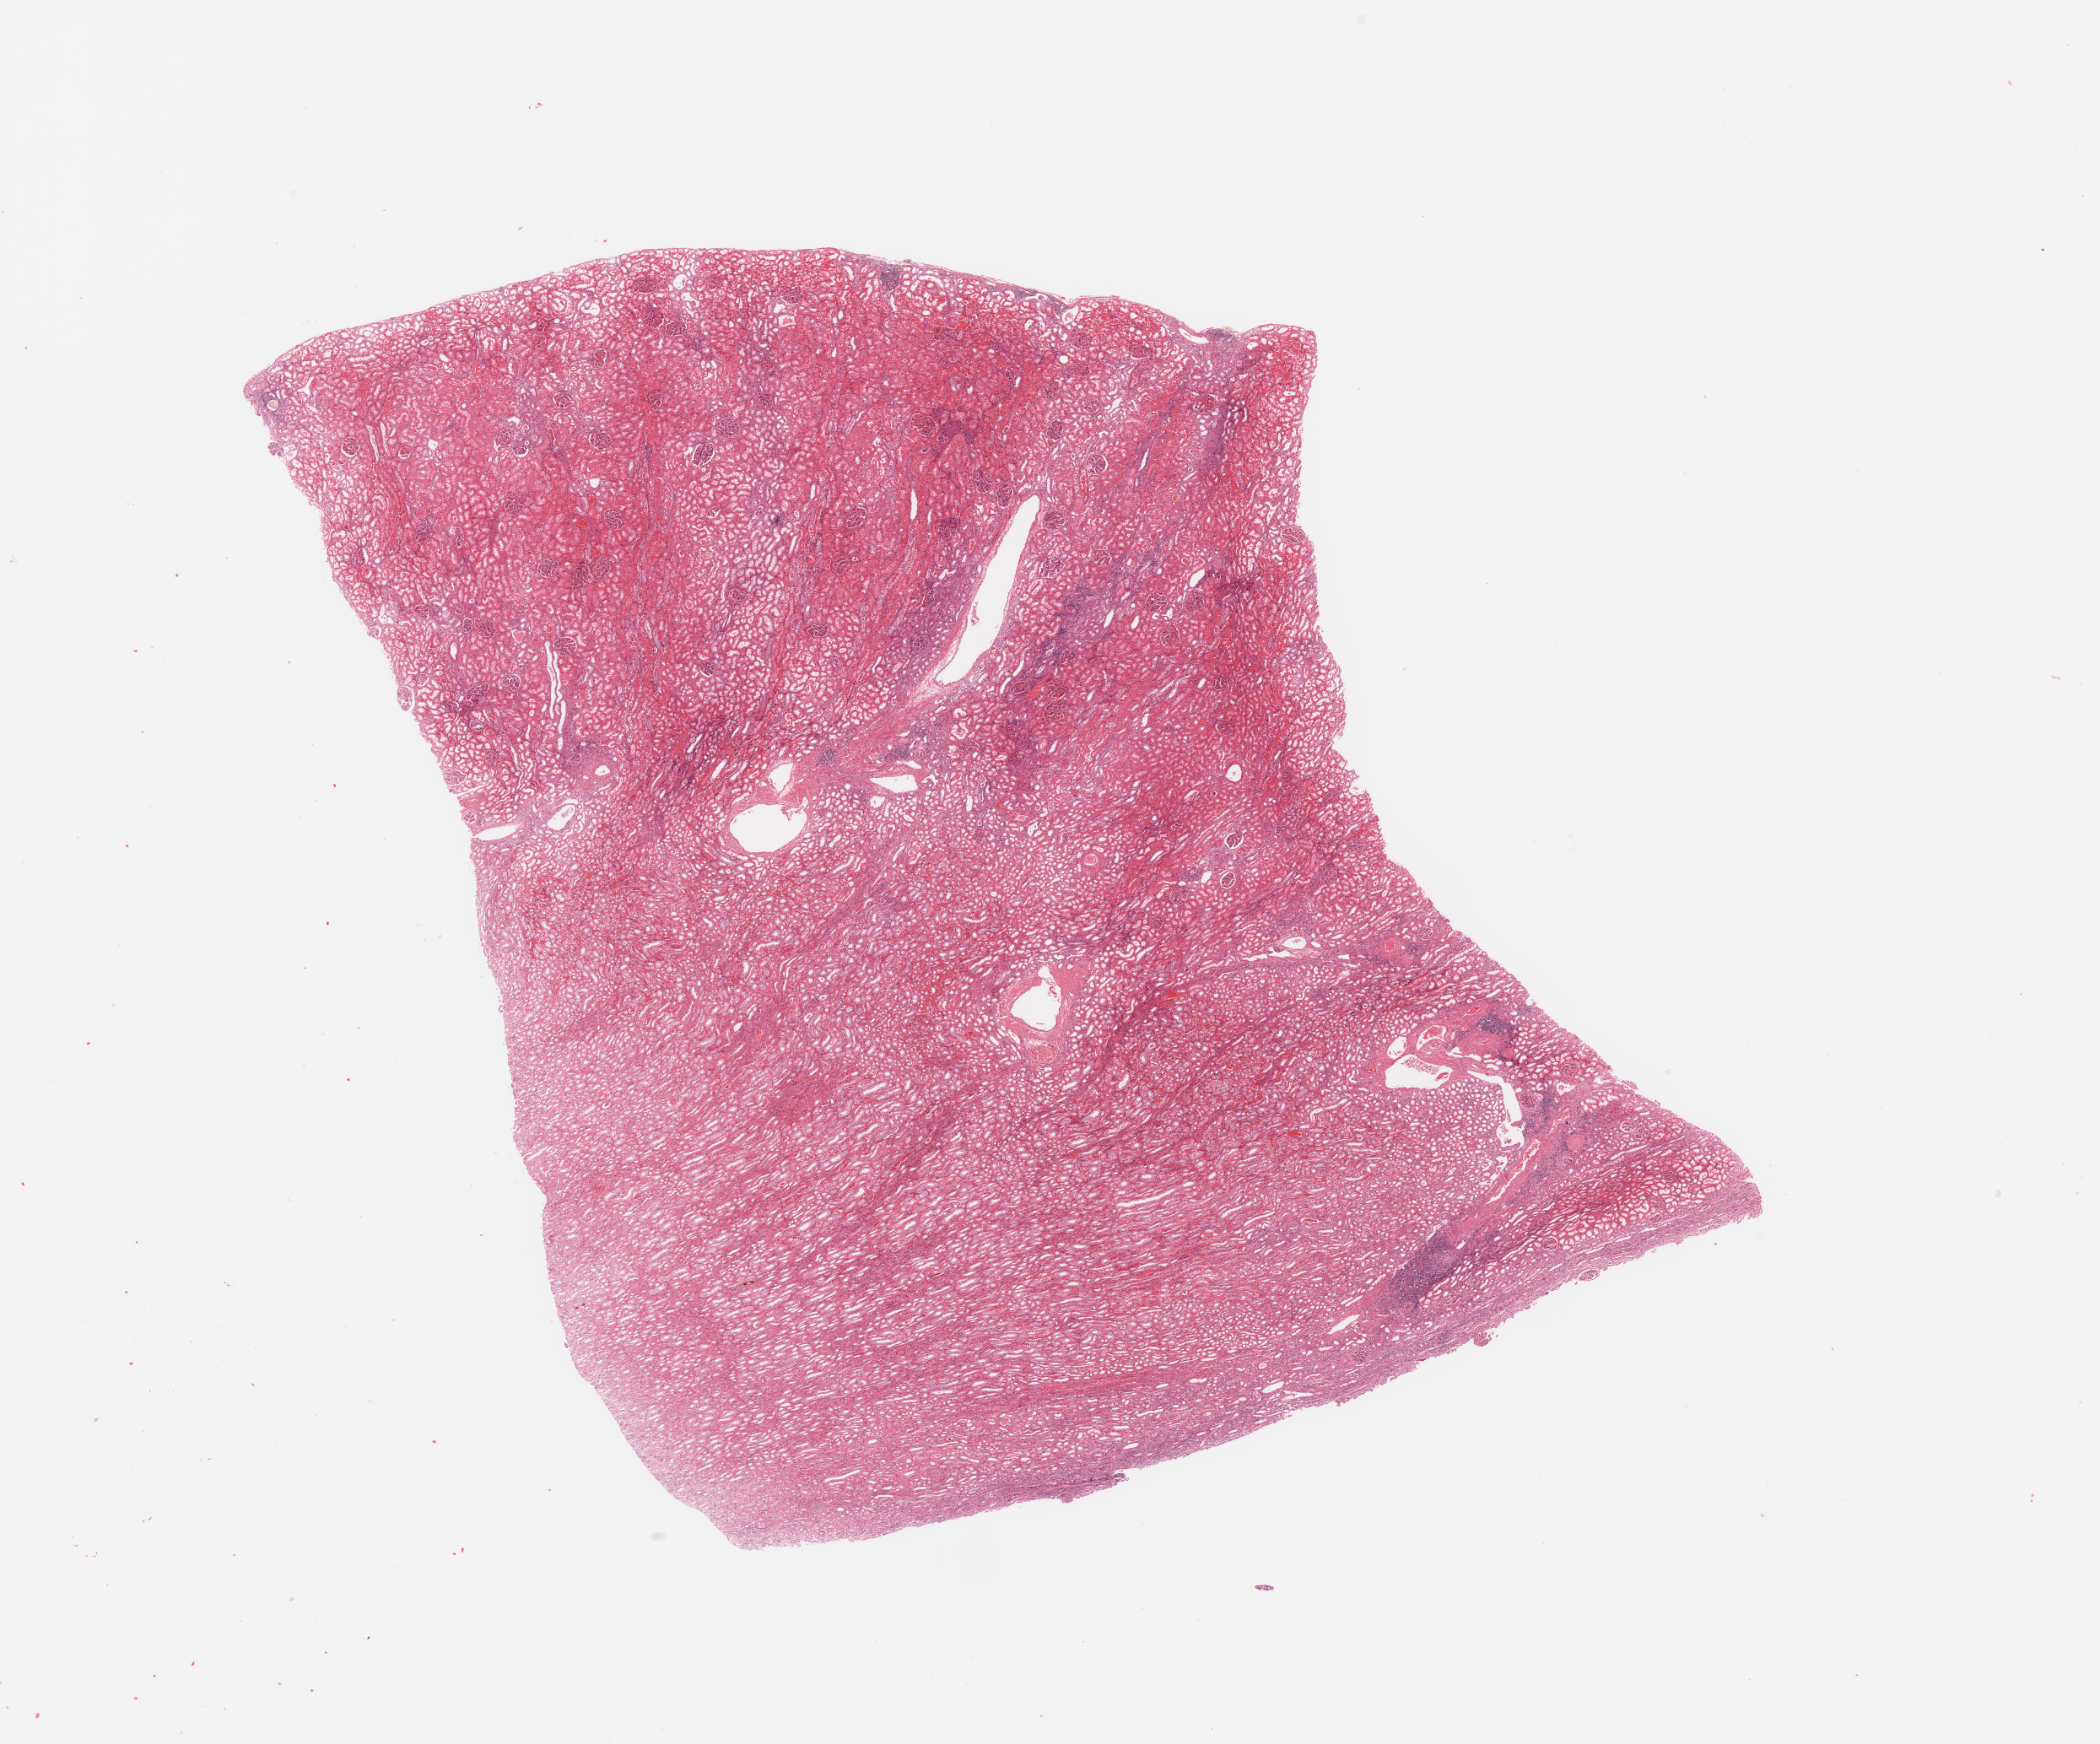
H&E-stained whole-slide image, shown as a low-resolution overview of the whole scanned area (about 19.7 x 16.4 mm); normal (non-tumour) tissue sample, sampled site: kidney. 55-year-old female patient.
• this section: normal (non-tumour) tissue from the same patient
• patient diagnosis: Renal cell carcinoma, NOS